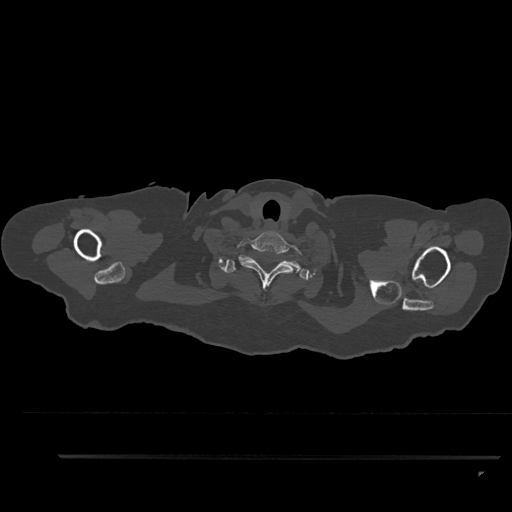
CT including the spine, one axial slice; position 784 of 797 along the scan axis; reconstruction kernel Br40s/3; bone window (W 1800 / L 400 HU); 0.5 mm slice thickness; 512 × 512 image matrix, field of view 408 × 408 mm. Female patient, age 44 years. From the clinical record (not read from this slice): primary cancer: renal; vertebrae with lytic lesions (as recorded): L1.
Annotated regions visible in this slice (semi-automatic segmentation, software-assisted and operator-edited):
- T1 vertebra: box from (x=221, y=255) to (x=309, y=280) px